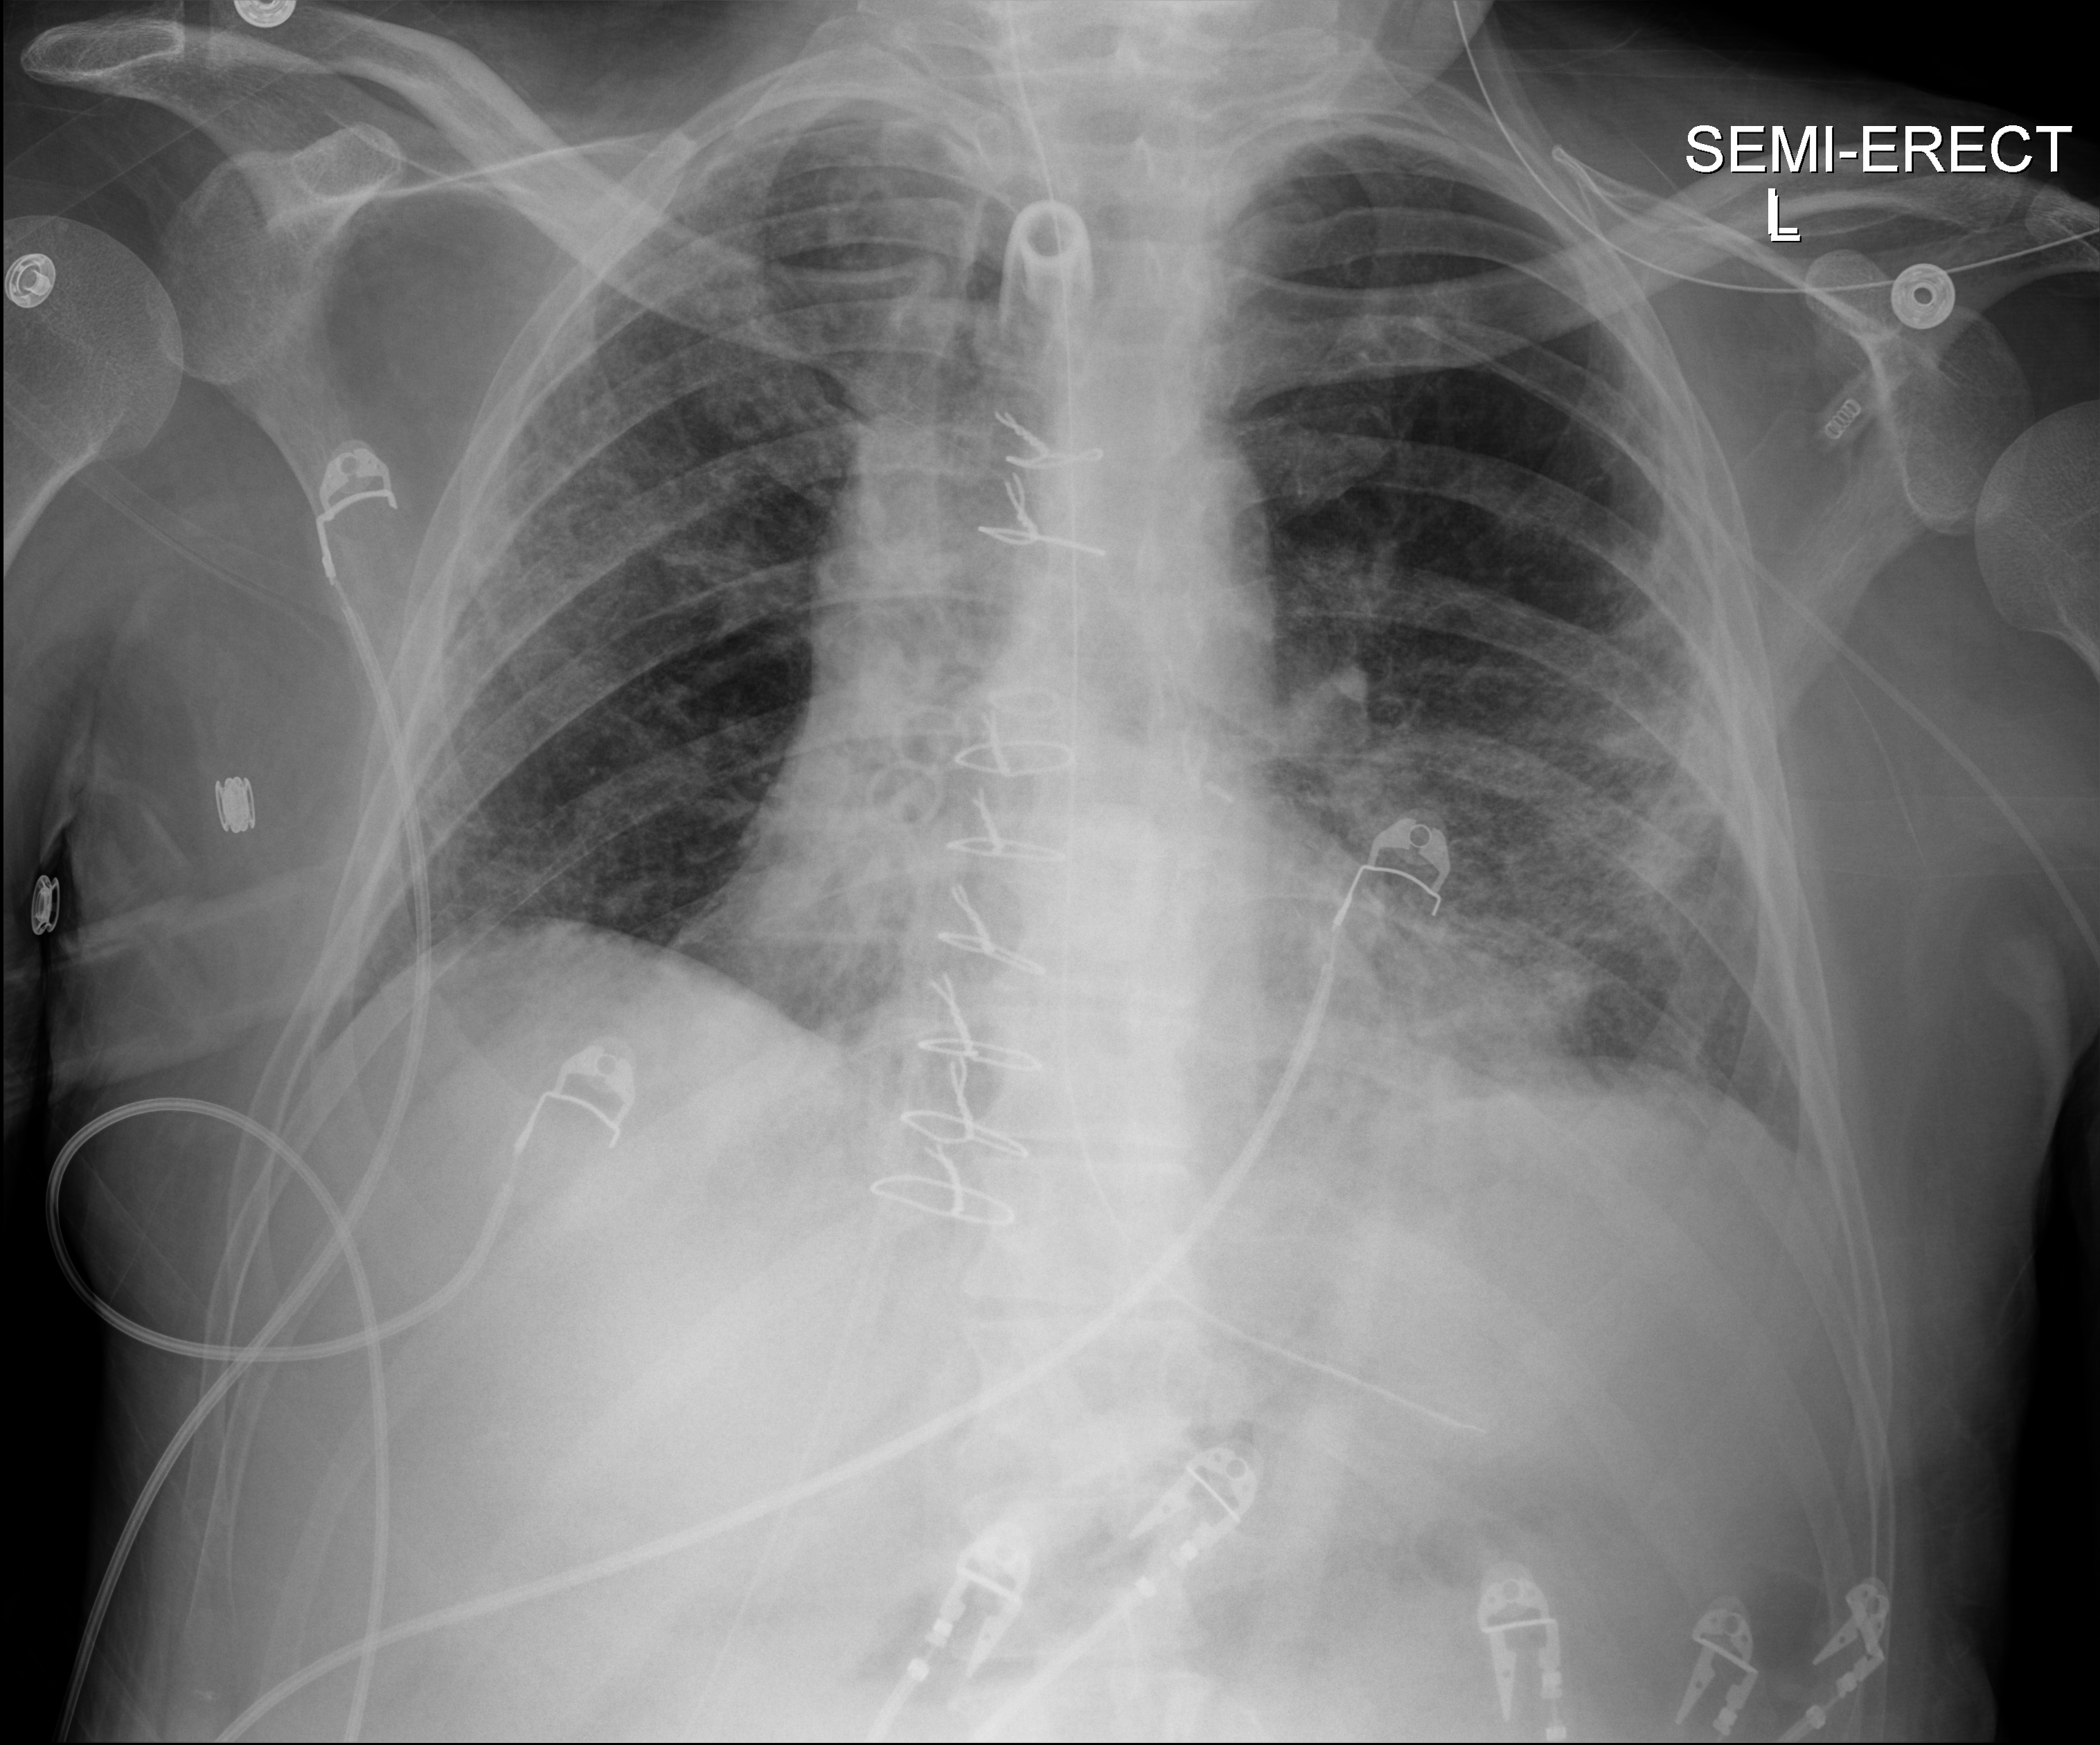
Portable chest radiograph; anteroposterior (AP) projection. Male patient hospitalised with COVID-19, age 18–59 years.
From the hospital-stay record, not from the radiograph (when in the stay this image was taken is not recorded):
- mechanically ventilated during this hospital stay: yes
- COPD (admission record): yes